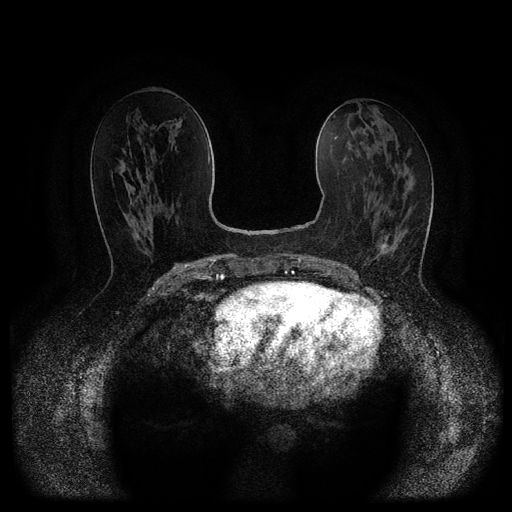
Breast MRI (dynamic contrast-enhanced, multi-phase), one axial slice; position 46 of 116 along the scan axis; dynamic contrast-enhanced series, time point 2 of 5 at this slice position (early post-contrast); 1.5 T; TE 2.6 ms, TR 5.4 ms; 512 × 512 image matrix. Patient: female, 61 years.
Annotated regions visible in this slice (semi-automatically segmented with operator editing):
- breast lesion (labelled 'tumour' in the annotation; benign lesions carry a separate 'benign' label): bounding box (x1, y1, x2, y2) in pixels: (381, 243, 386, 253)